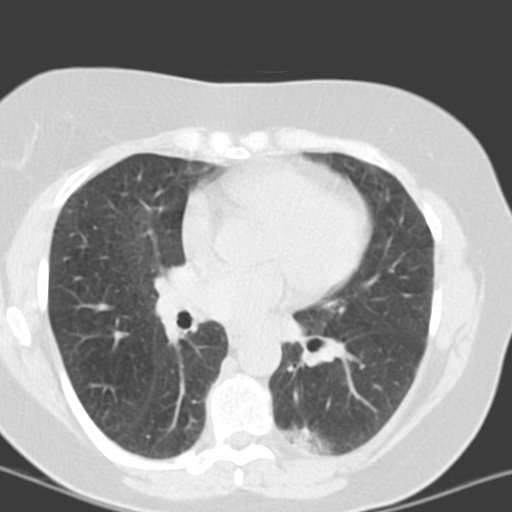
Axial slice from a low-dose chest CT screening exam. Third screening round (two years after baseline). Lung window (W 1500 / L -600 HU). Standard (soft-tissue) reconstruction kernel (B). 512 × 512 image matrix, field of view 290 × 290 mm. Female, age 55 years at enrolment. Current smoker at enrolment.
Expert reader's lesion annotation, bounding box (x1, y1, x2, y2) in pixels: (279, 406, 360, 462). The screening reader recorded 6 non-calcified nodules or masses ≥4 mm on this exam (left lower lobe, left lower lobe, left upper lobe, lingula, lingula, right middle lobe); which of them this box marks is not recorded. Official screen result: positive, no significant change: stable abnormalities potentially related to lung cancer, unchanged since the prior screening exam. Later outcome: lung cancer diagnosed 357 days after this screen — adenocarcinoma with mixed subtypes, left lower lobe, poorly differentiated (G3), stage IA (AJCC 6th edition), 21 mm at pathology.